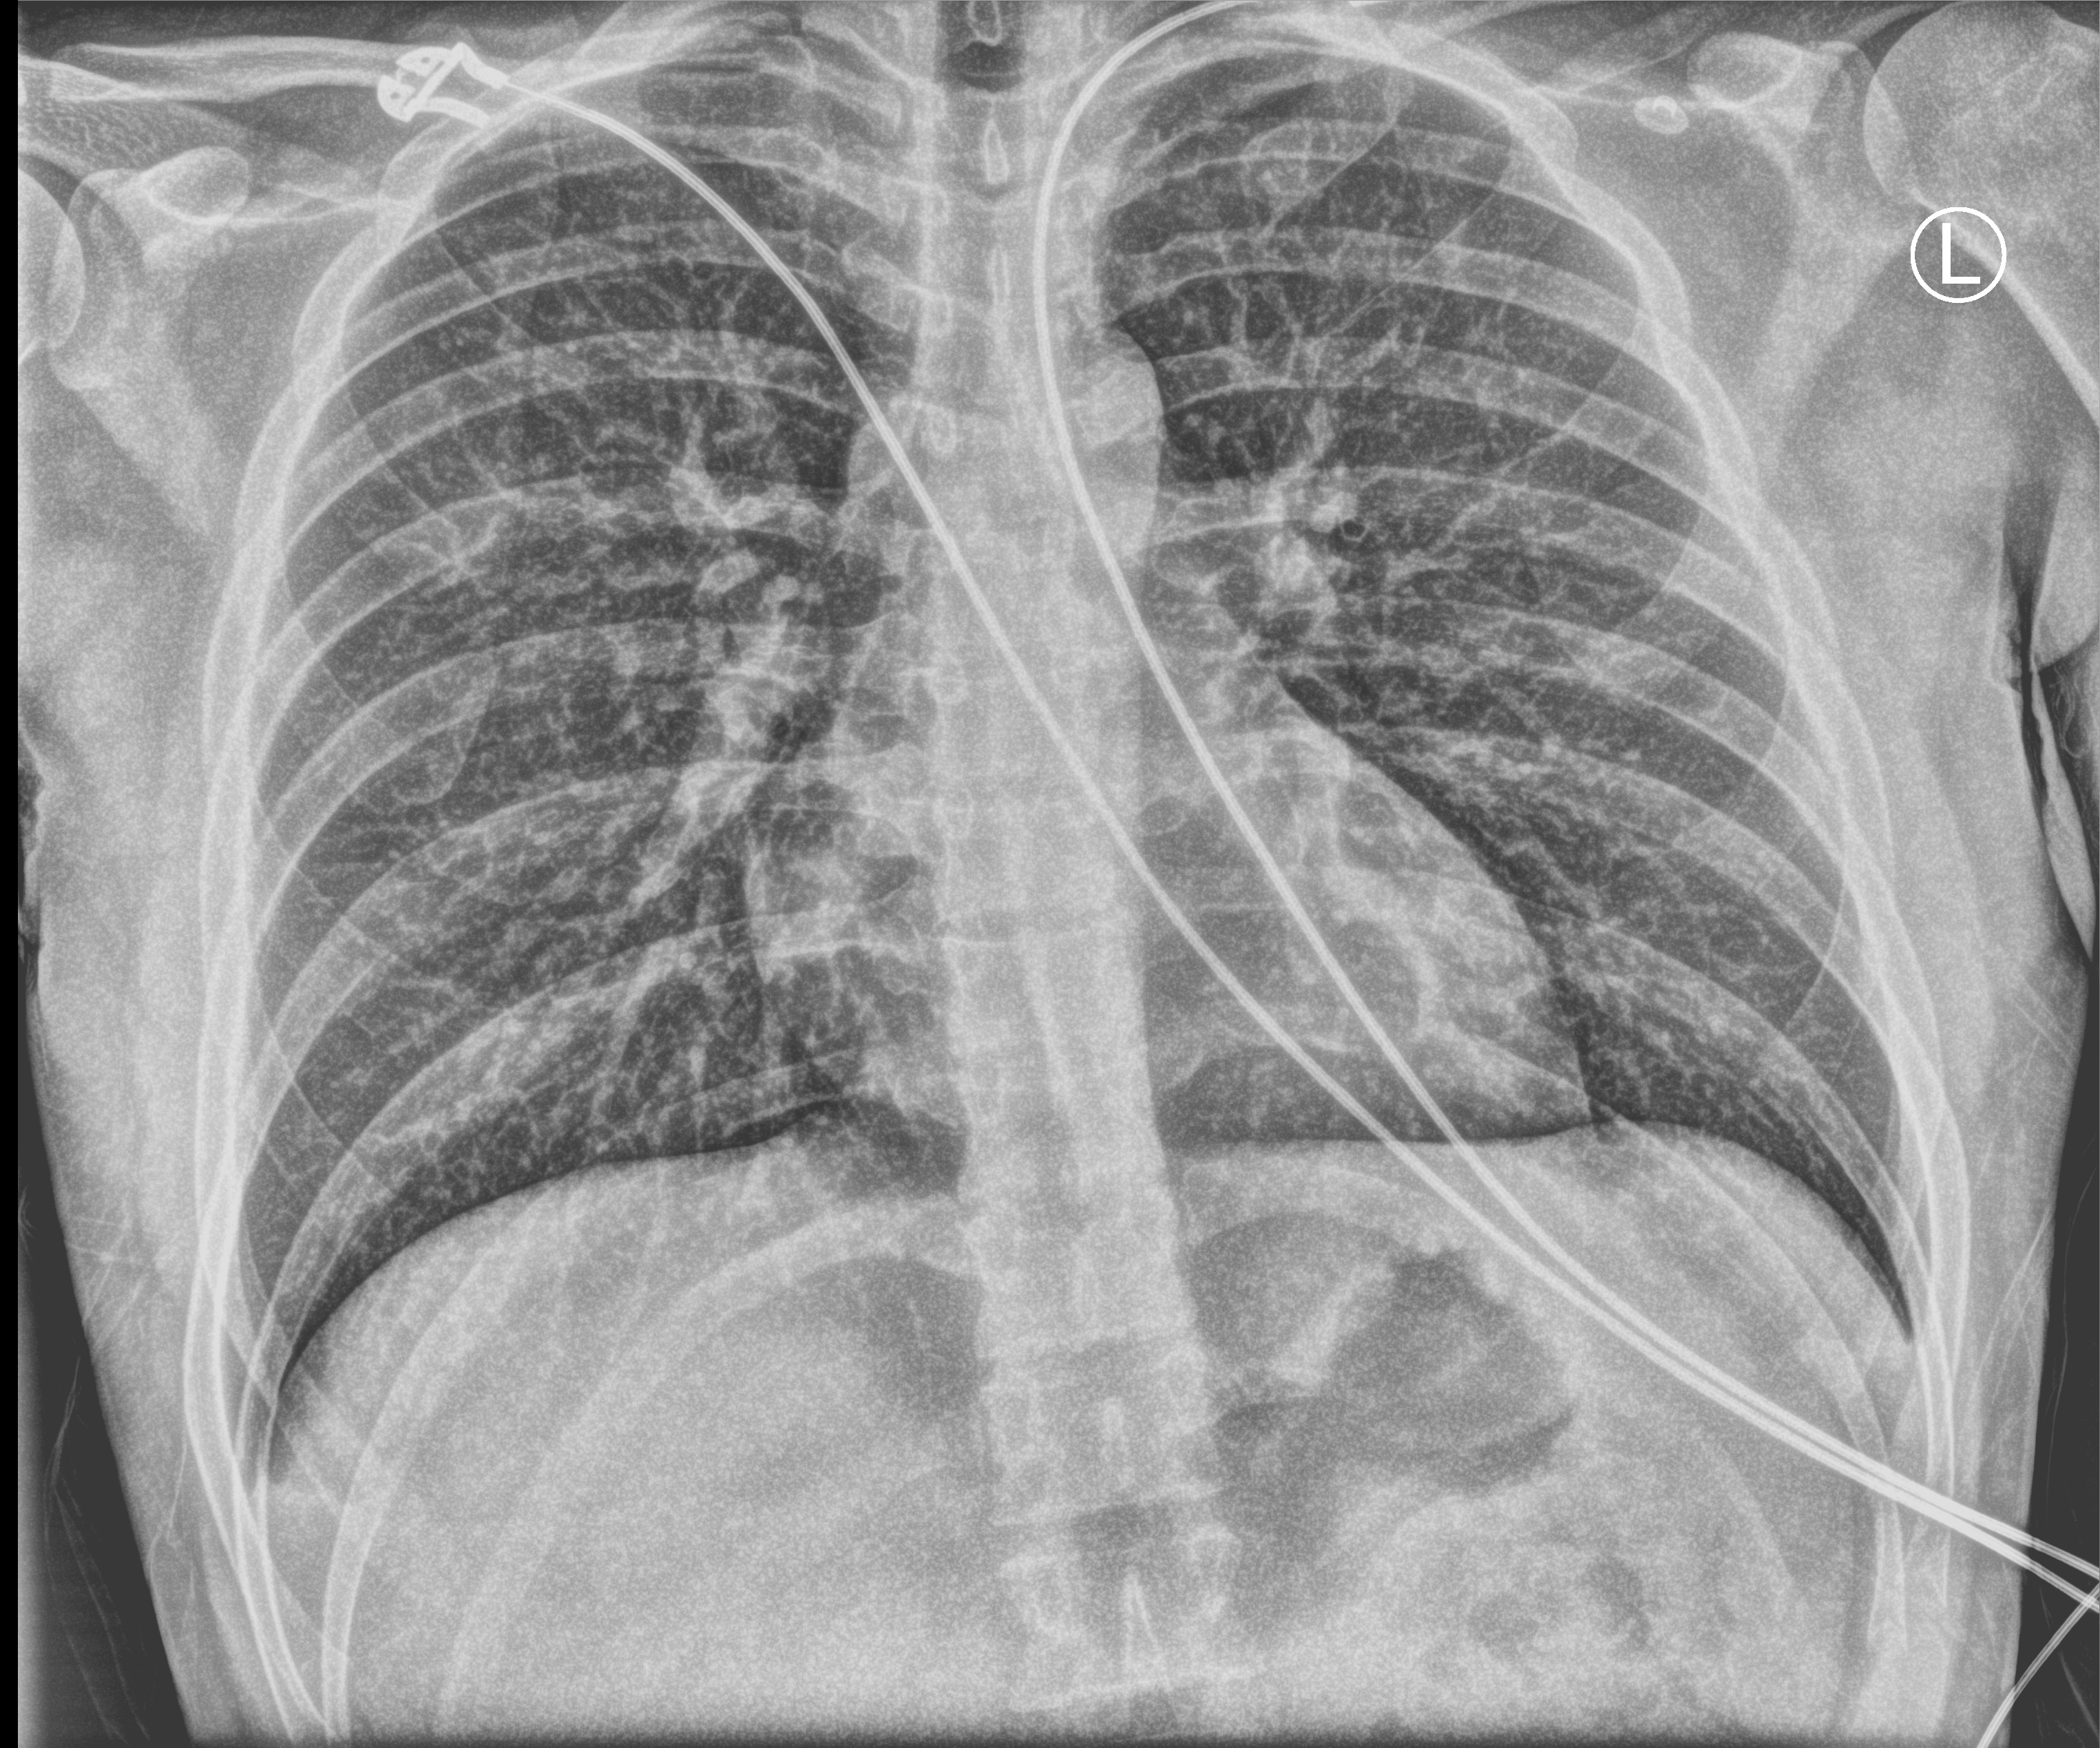
Bedside chest radiograph (computed radiography). Male patient hospitalised with COVID-19, age 18–59 years.
From the hospital-stay record, not from the radiograph (when in the stay this image was taken is not recorded):
- mechanically ventilated during this hospital stay: no